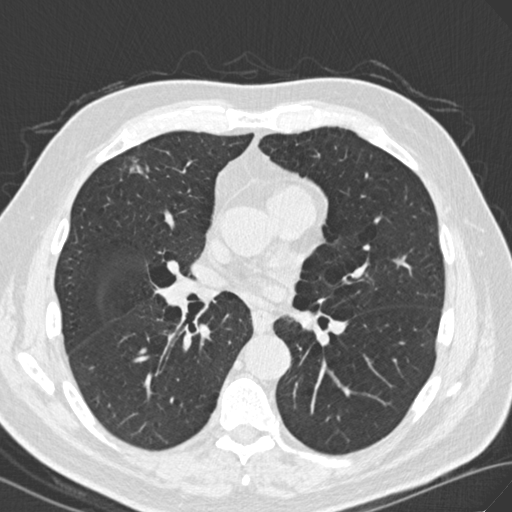
Low-dose screening chest CT, one axial slice; slice 86 of 171 in the series (ordered by position); reconstruction kernel B30f; lung window (W 1500 / L -600 HU); 2 mm slice thickness; 512 × 512 image matrix, field of view 352 × 352 mm.
Structures marked on this image (manually delineated by an expert):
- lesion 1 (tumor, upper lobe of right lung): bounding box (x1, y1, x2, y2) in pixels: (128, 157, 146, 177)